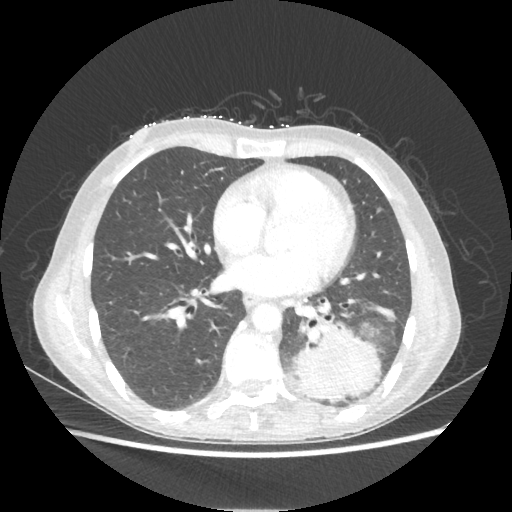
Chest CT, one axial slice; slice 95 of 221 in the series (ordered by position); reconstruction kernel STANDARD; 80 kVp; lung window (W 1500 / L -600 HU); 1.25 mm slice thickness; 512 × 512 image matrix, field of view 360 × 360 mm. Patient: female, 53 years. From the clinical record (not read from this slice): clinical TNM (as recorded): T3 N0 M0.
Outlined on this slice (bounding box drawn by a radiologist):
- lung tumour (recorded histology: adenocarcinoma): box from (x=289, y=322) to (x=380, y=403) px